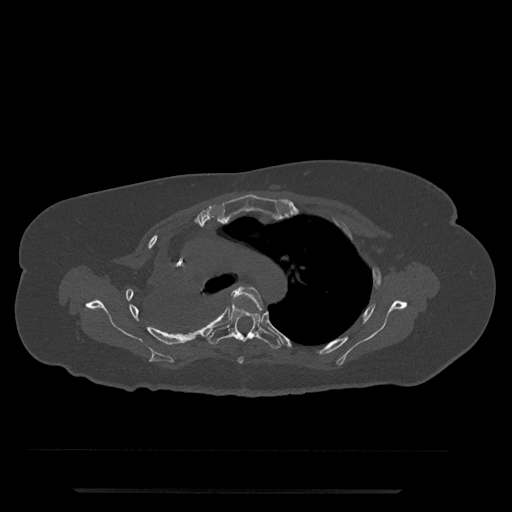
CT including the spine, one axial slice; slice 558 of 797 in the series (ordered by position); reconstruction kernel Br40s/3; bone window (W 1800 / L 400 HU); 0.5 mm slice thickness; 512 × 512 image matrix, field of view 440 × 440 mm. Patient: female, 51 years. From the clinical record (not read from this slice): primary cancer: neuro; vertebrae with lytic lesions (as recorded): T8.
Structures marked on this image (semi-automatically segmented with operator editing):
- T4 vertebra: bounding box <232,286,263,364> (left, top, right, bottom; pixels)
- T5 vertebra: <207,303,282,349>